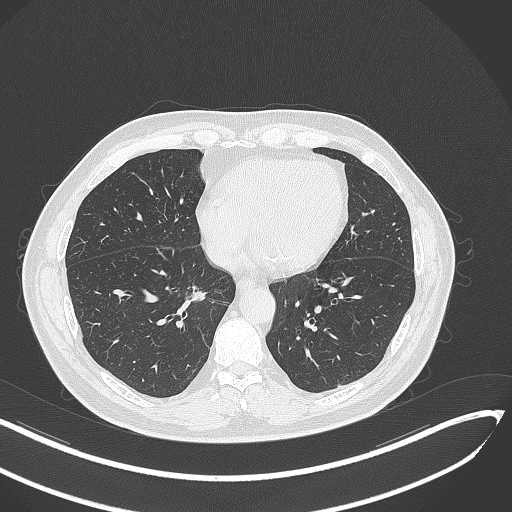
Chest CT, one axial slice; slice 137 of 429 in the series (ordered by position); reconstruction kernel B70f; 120 kVp; lung window (W 1500 / L -600 HU); 512 × 512 image matrix, field of view 400 × 400 mm. Male patient, age 62 years. Case-level facts recorded for this patient, not image findings: clinical TNM (as recorded): T1b N0 M0.
Structures marked on this image (bounding box drawn by a radiologist):
- lung tumour (recorded histology: adenocarcinoma): bounding box [x1, y1, x2, y2] px = [184, 281, 209, 306]